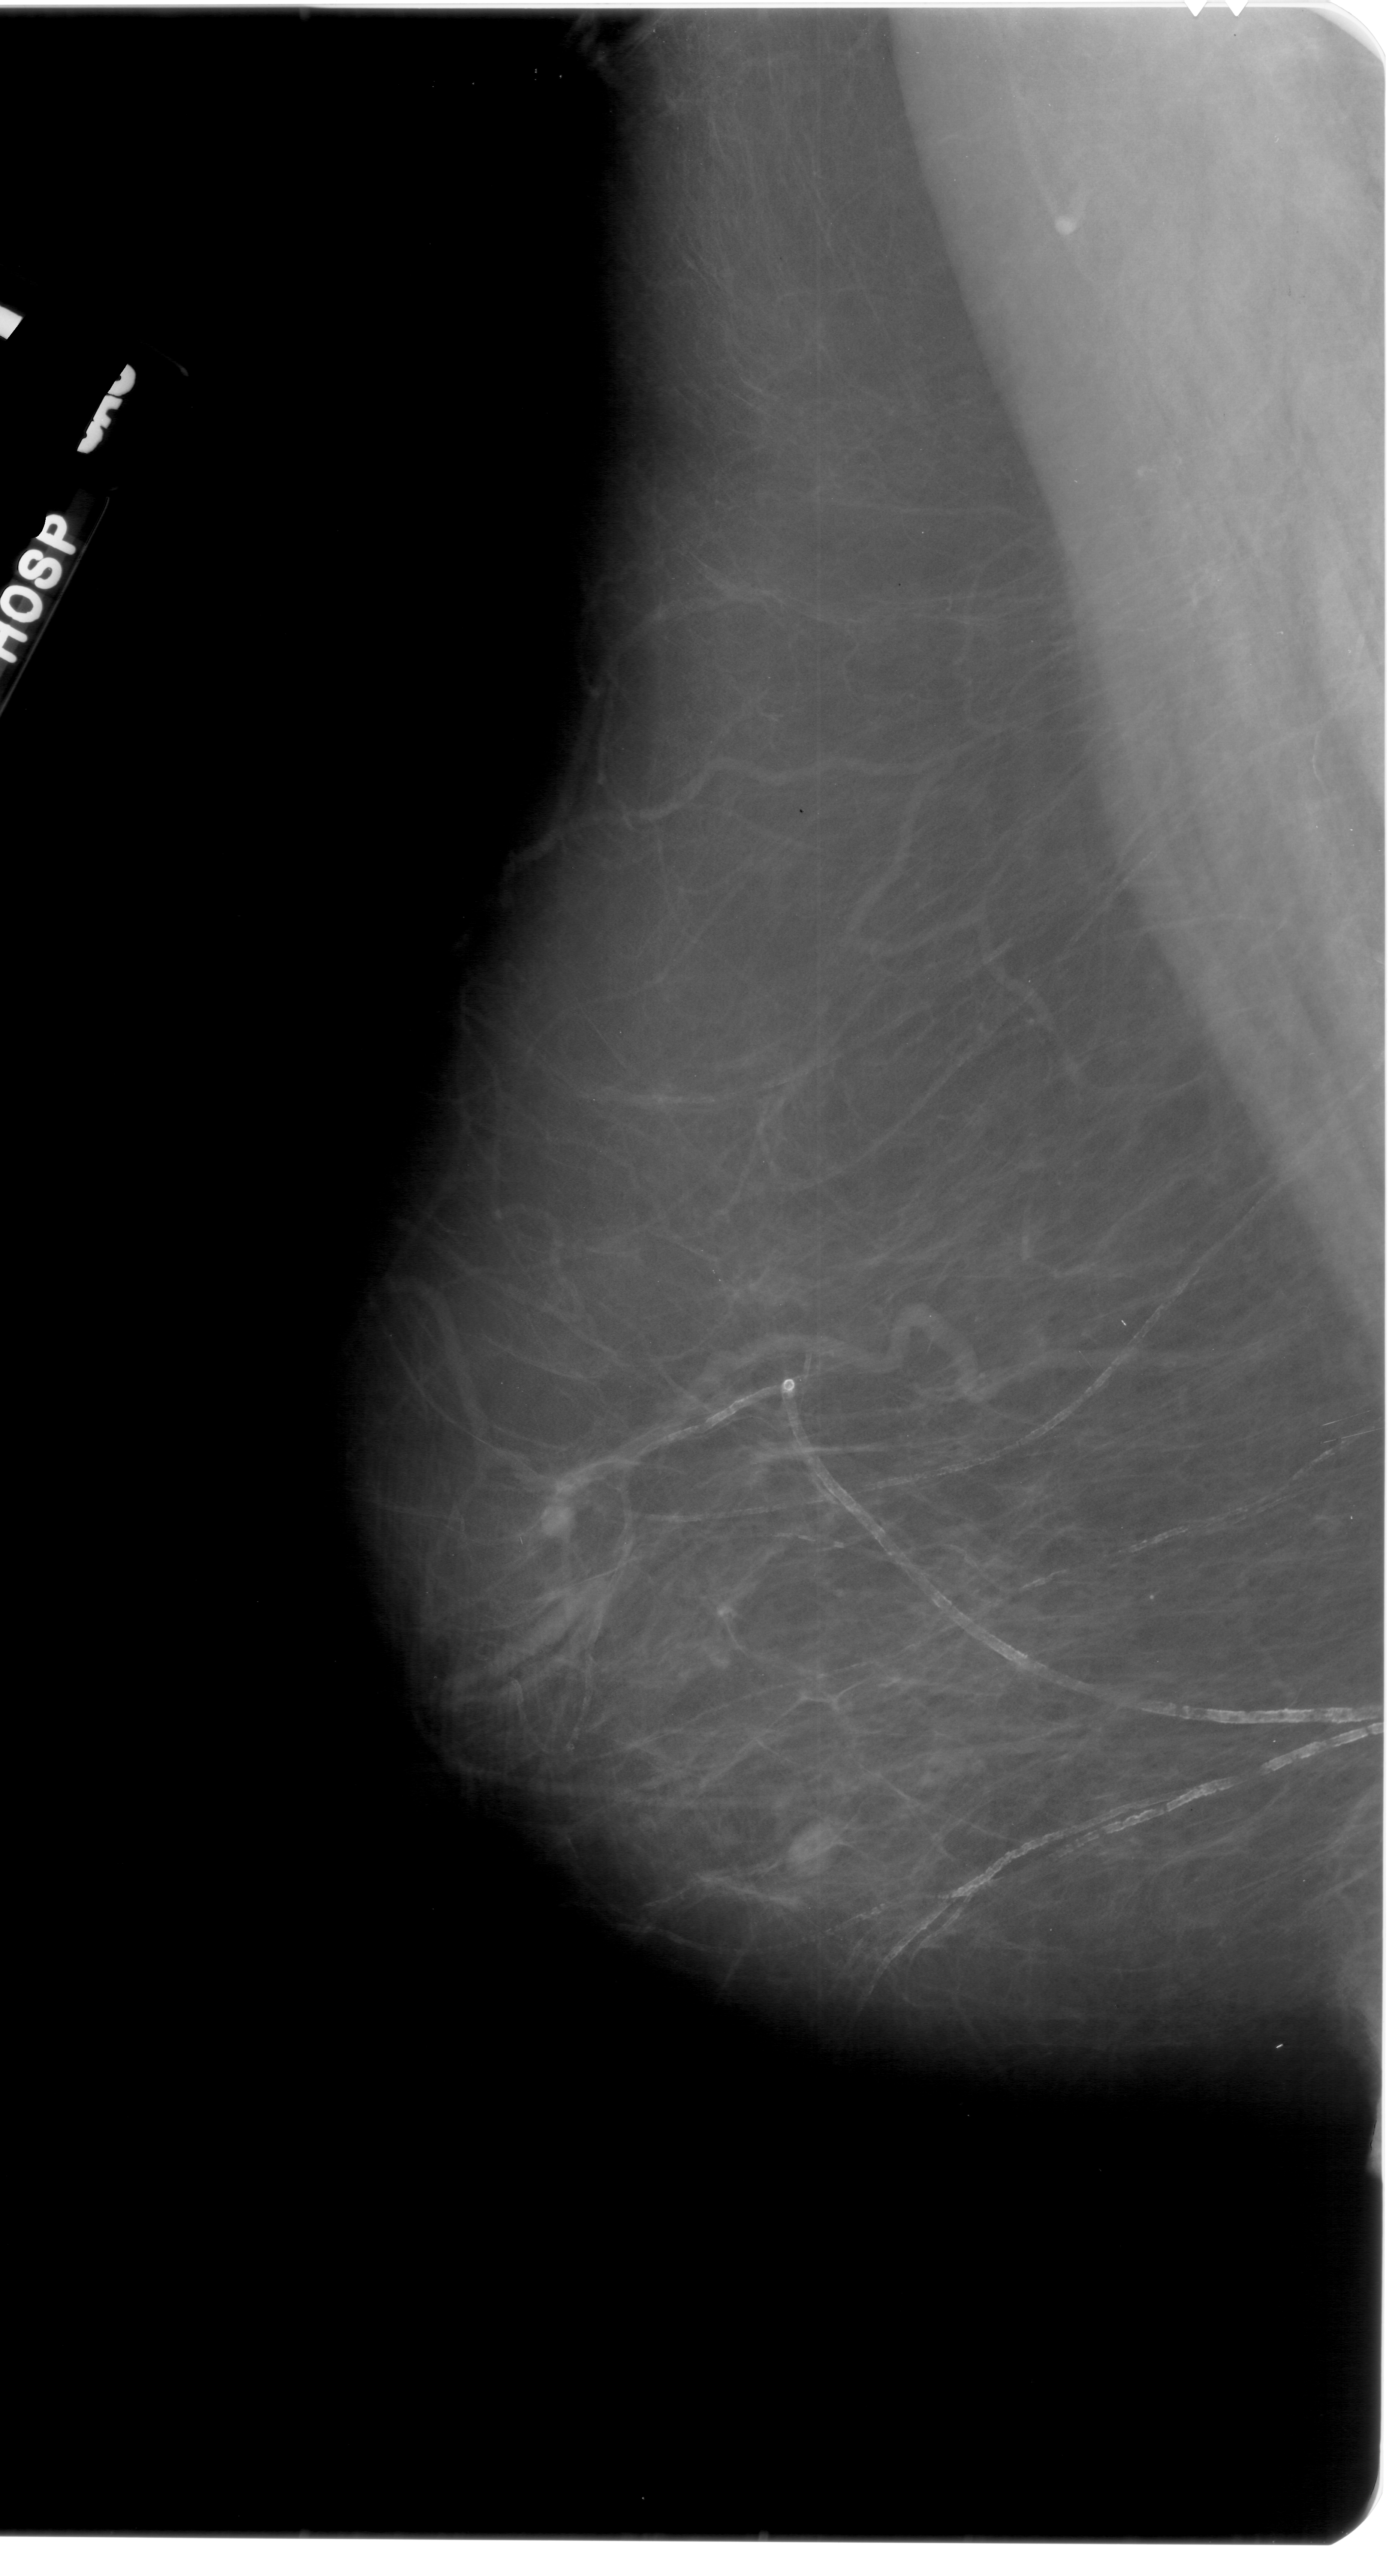
Digitized screen-film mammogram; left breast; MLO view; BI-RADS breast density category 2 (scale 1–4).
- Mass, shape oval, margins circumscribed; BI-RADS assessment category 4; pathology (as recorded): malignant.